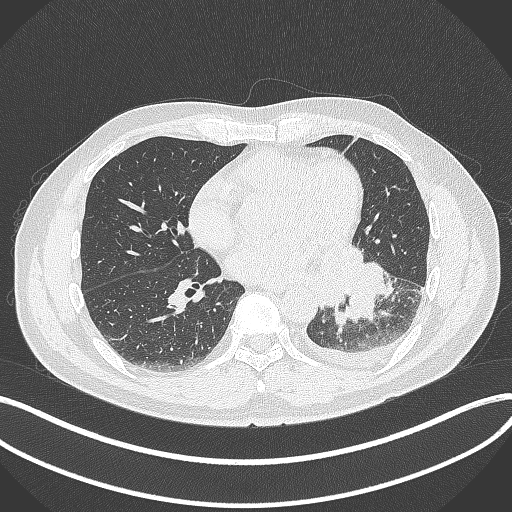
Chest CT, one axial slice. Slice 156 of 342 in the series (ordered by position). Lung window (W 1500 / L -600 HU). 1 mm slice thickness. 512 × 512 image matrix. Patient: male, 58 years. Case-level facts recorded for this patient, not image findings: clinical TNM (as recorded): T3 N1 M1b.
Annotated regions visible in this slice (bounding box drawn by a radiologist):
- lung tumour (recorded histology: small cell carcinoma): bounding box <318,248,388,324> (left, top, right, bottom; pixels)